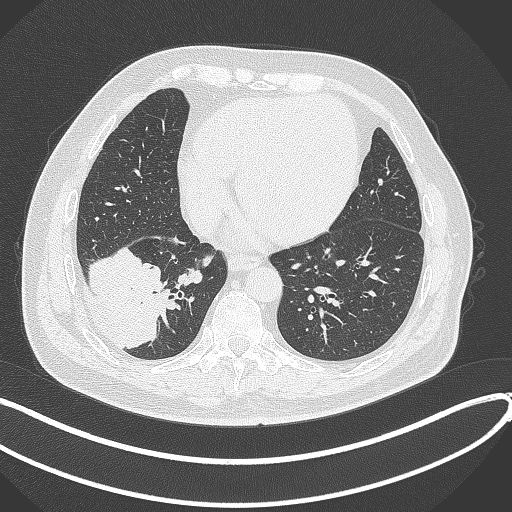
Chest CT, one axial slice. Position 116 of 360 along the scan axis. Lung window (W 1500 / L -600 HU). 512 × 512 image matrix, field of view 400 × 400 mm. Male patient, age 59 years.
Outlined on this slice (rectangle marked by the reading radiologist):
- lung tumour (recorded histology: adenocarcinoma): box from (x=88, y=243) to (x=182, y=350) px